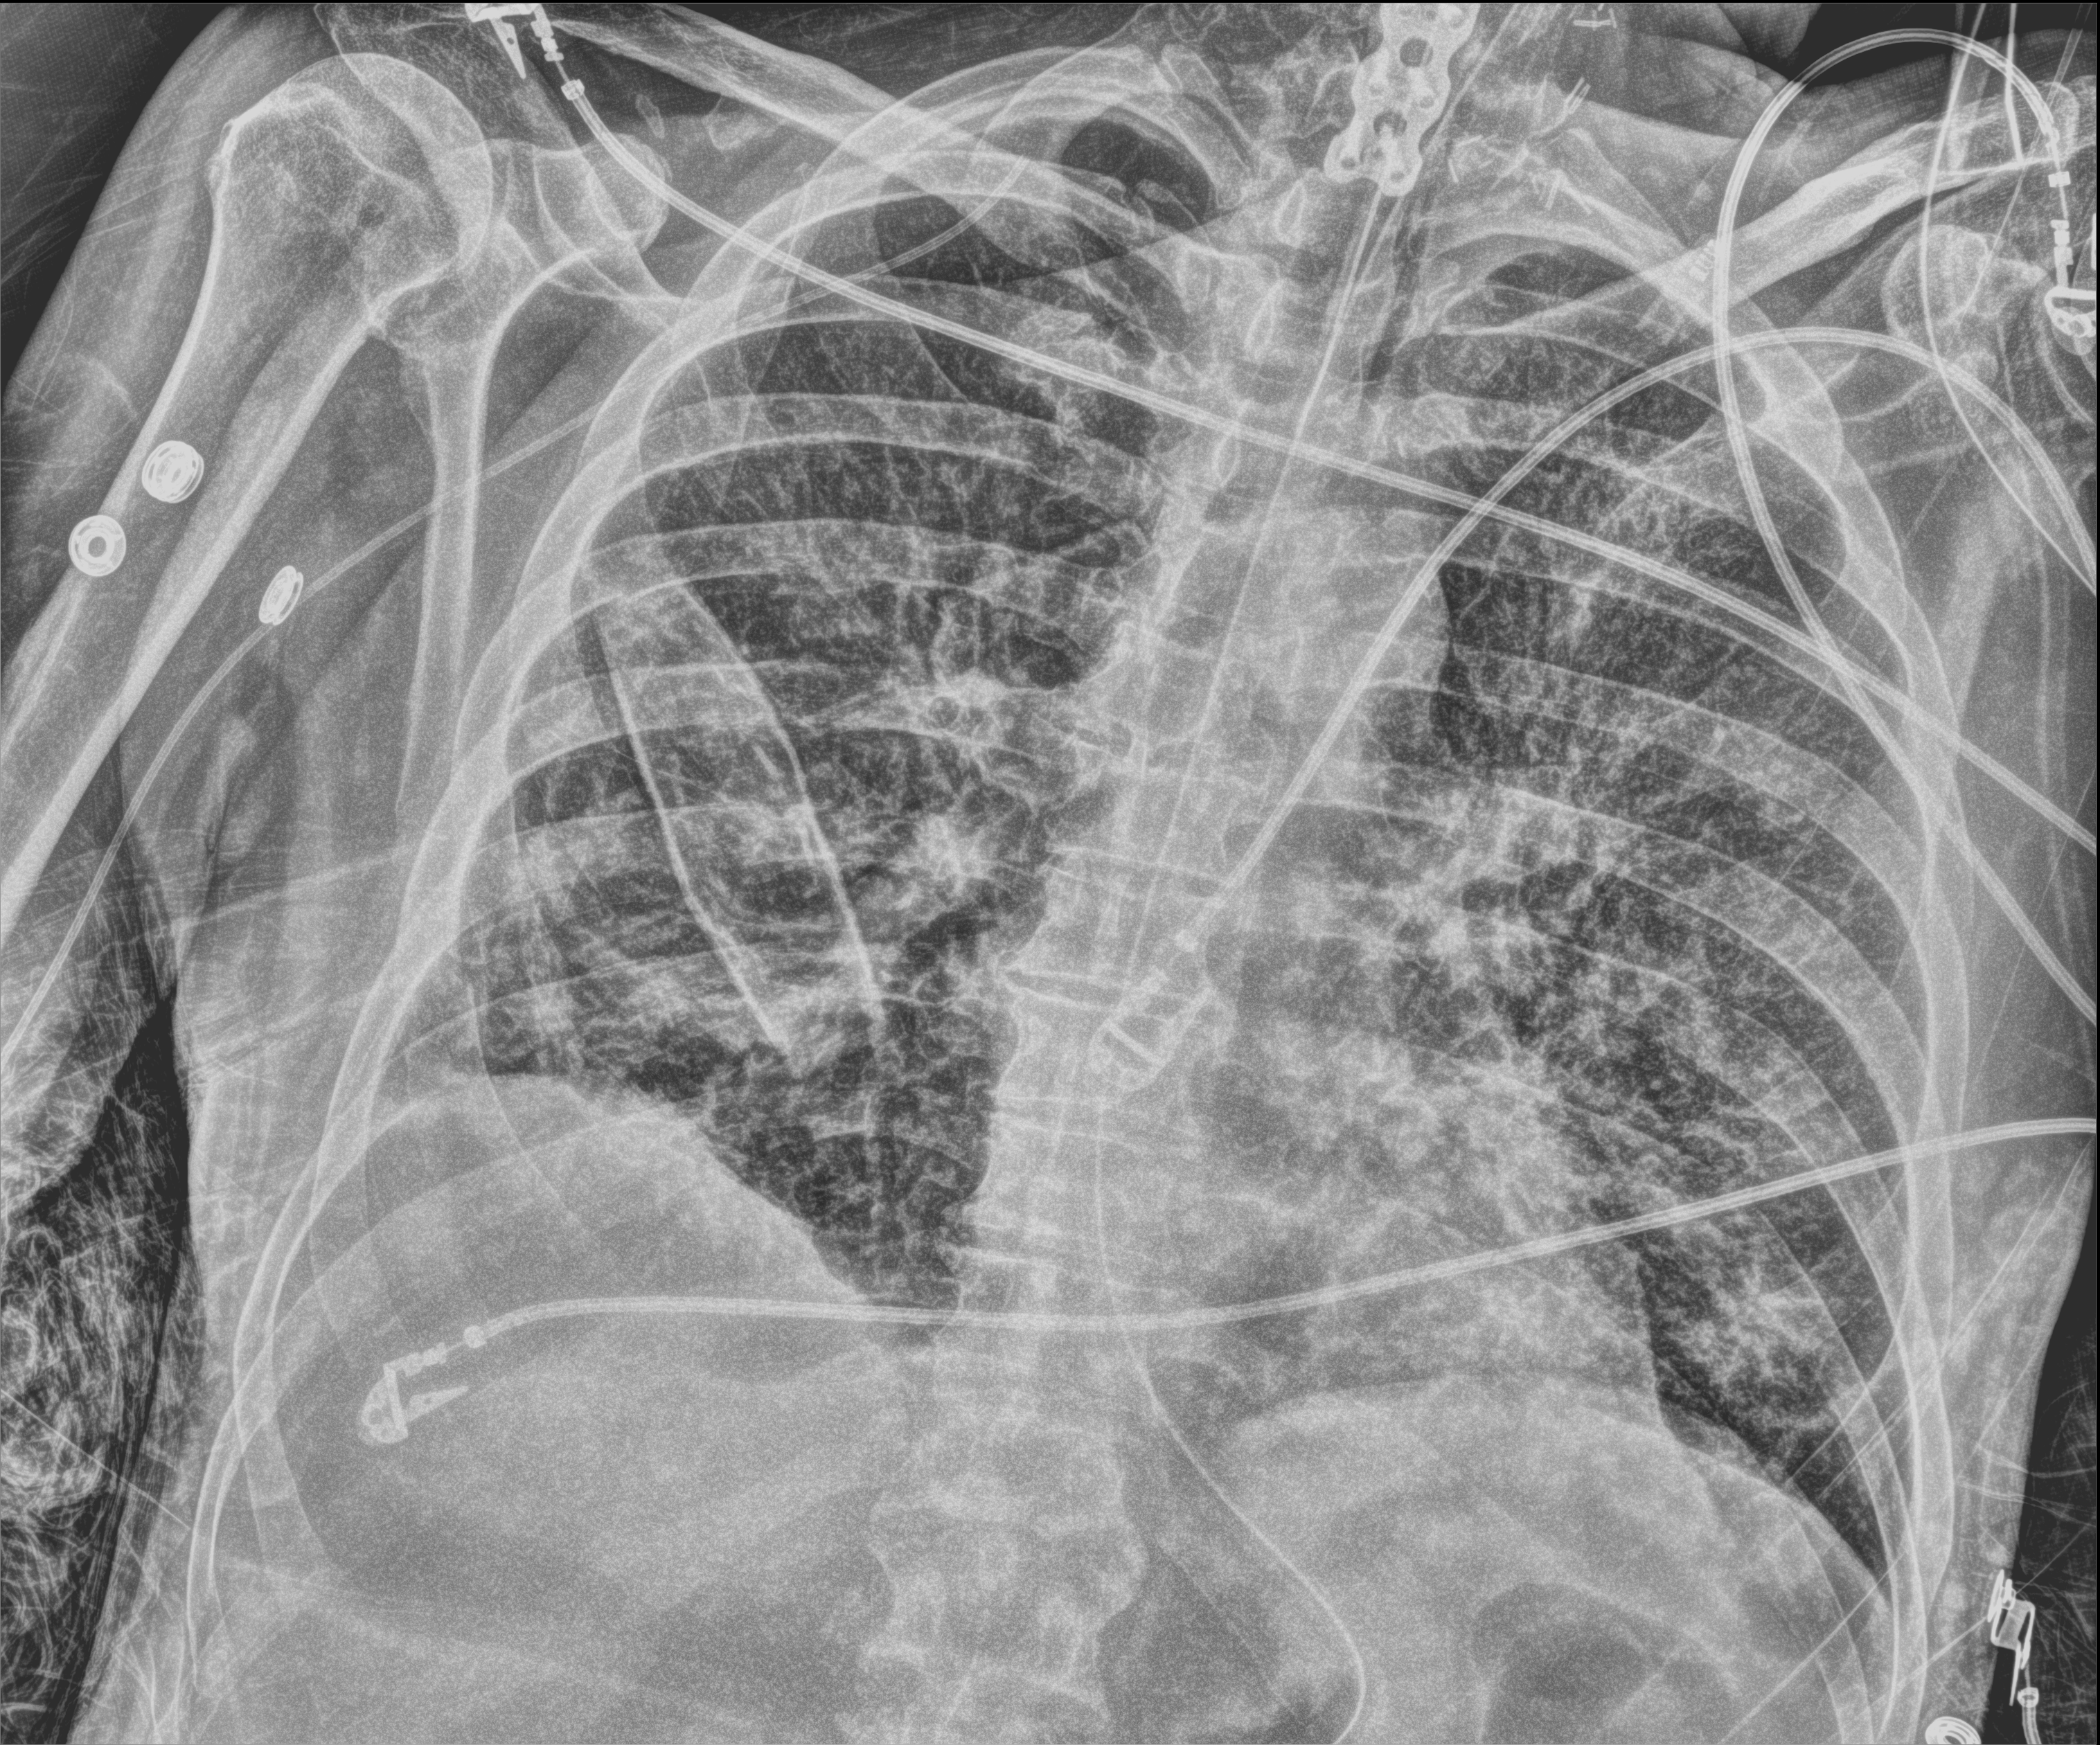
Portable chest radiograph, anteroposterior (AP) projection. Patient hospitalised with COVID-19; male, aged 60–74 years.
Admission-level facts for this patient (not findings on this image; timing relative to this image not recorded): mechanically ventilated during this hospital stay: yes; admitted to intensive care during this hospital stay: yes.